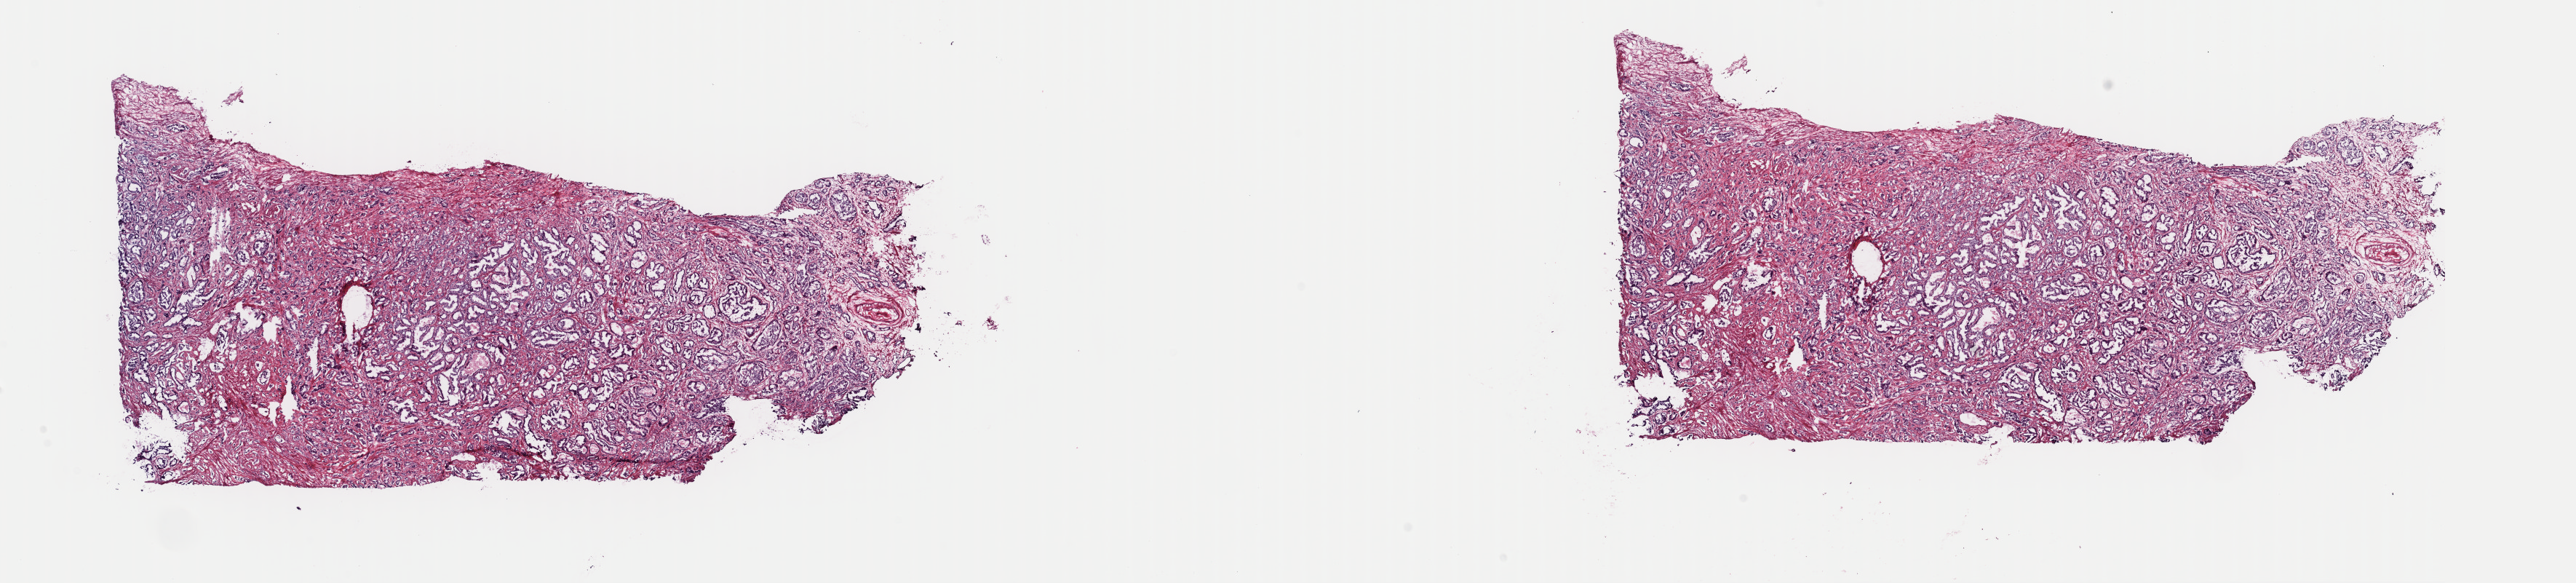
Whole-slide histology image, Hematoxylin and eosin (H&E) stained, shown as a low-resolution overview of the whole scanned area (about 28.0 x 6.3 mm, slide scanned at 40x). Frozen section from the top of the tissue portion. Prostate, primary tumour sample. Male, age 60 years at initial diagnosis. Gleason score: 7 (4+3). Pathologist review of this section (percent, as recorded): tumour cells 70%, tumour nuclei 70%, normal cells 5%, stromal cells 25%, necrosis 0%. Inflammatory infiltration, as recorded: lymphocyte infiltration 40%, monocyte infiltration 20%, neutrophil infiltration 20%.
Diagnosis: Adenocarcinoma, NOS (prostate gland). Lymph nodes positive (case pathology): 0 of 8 examined.